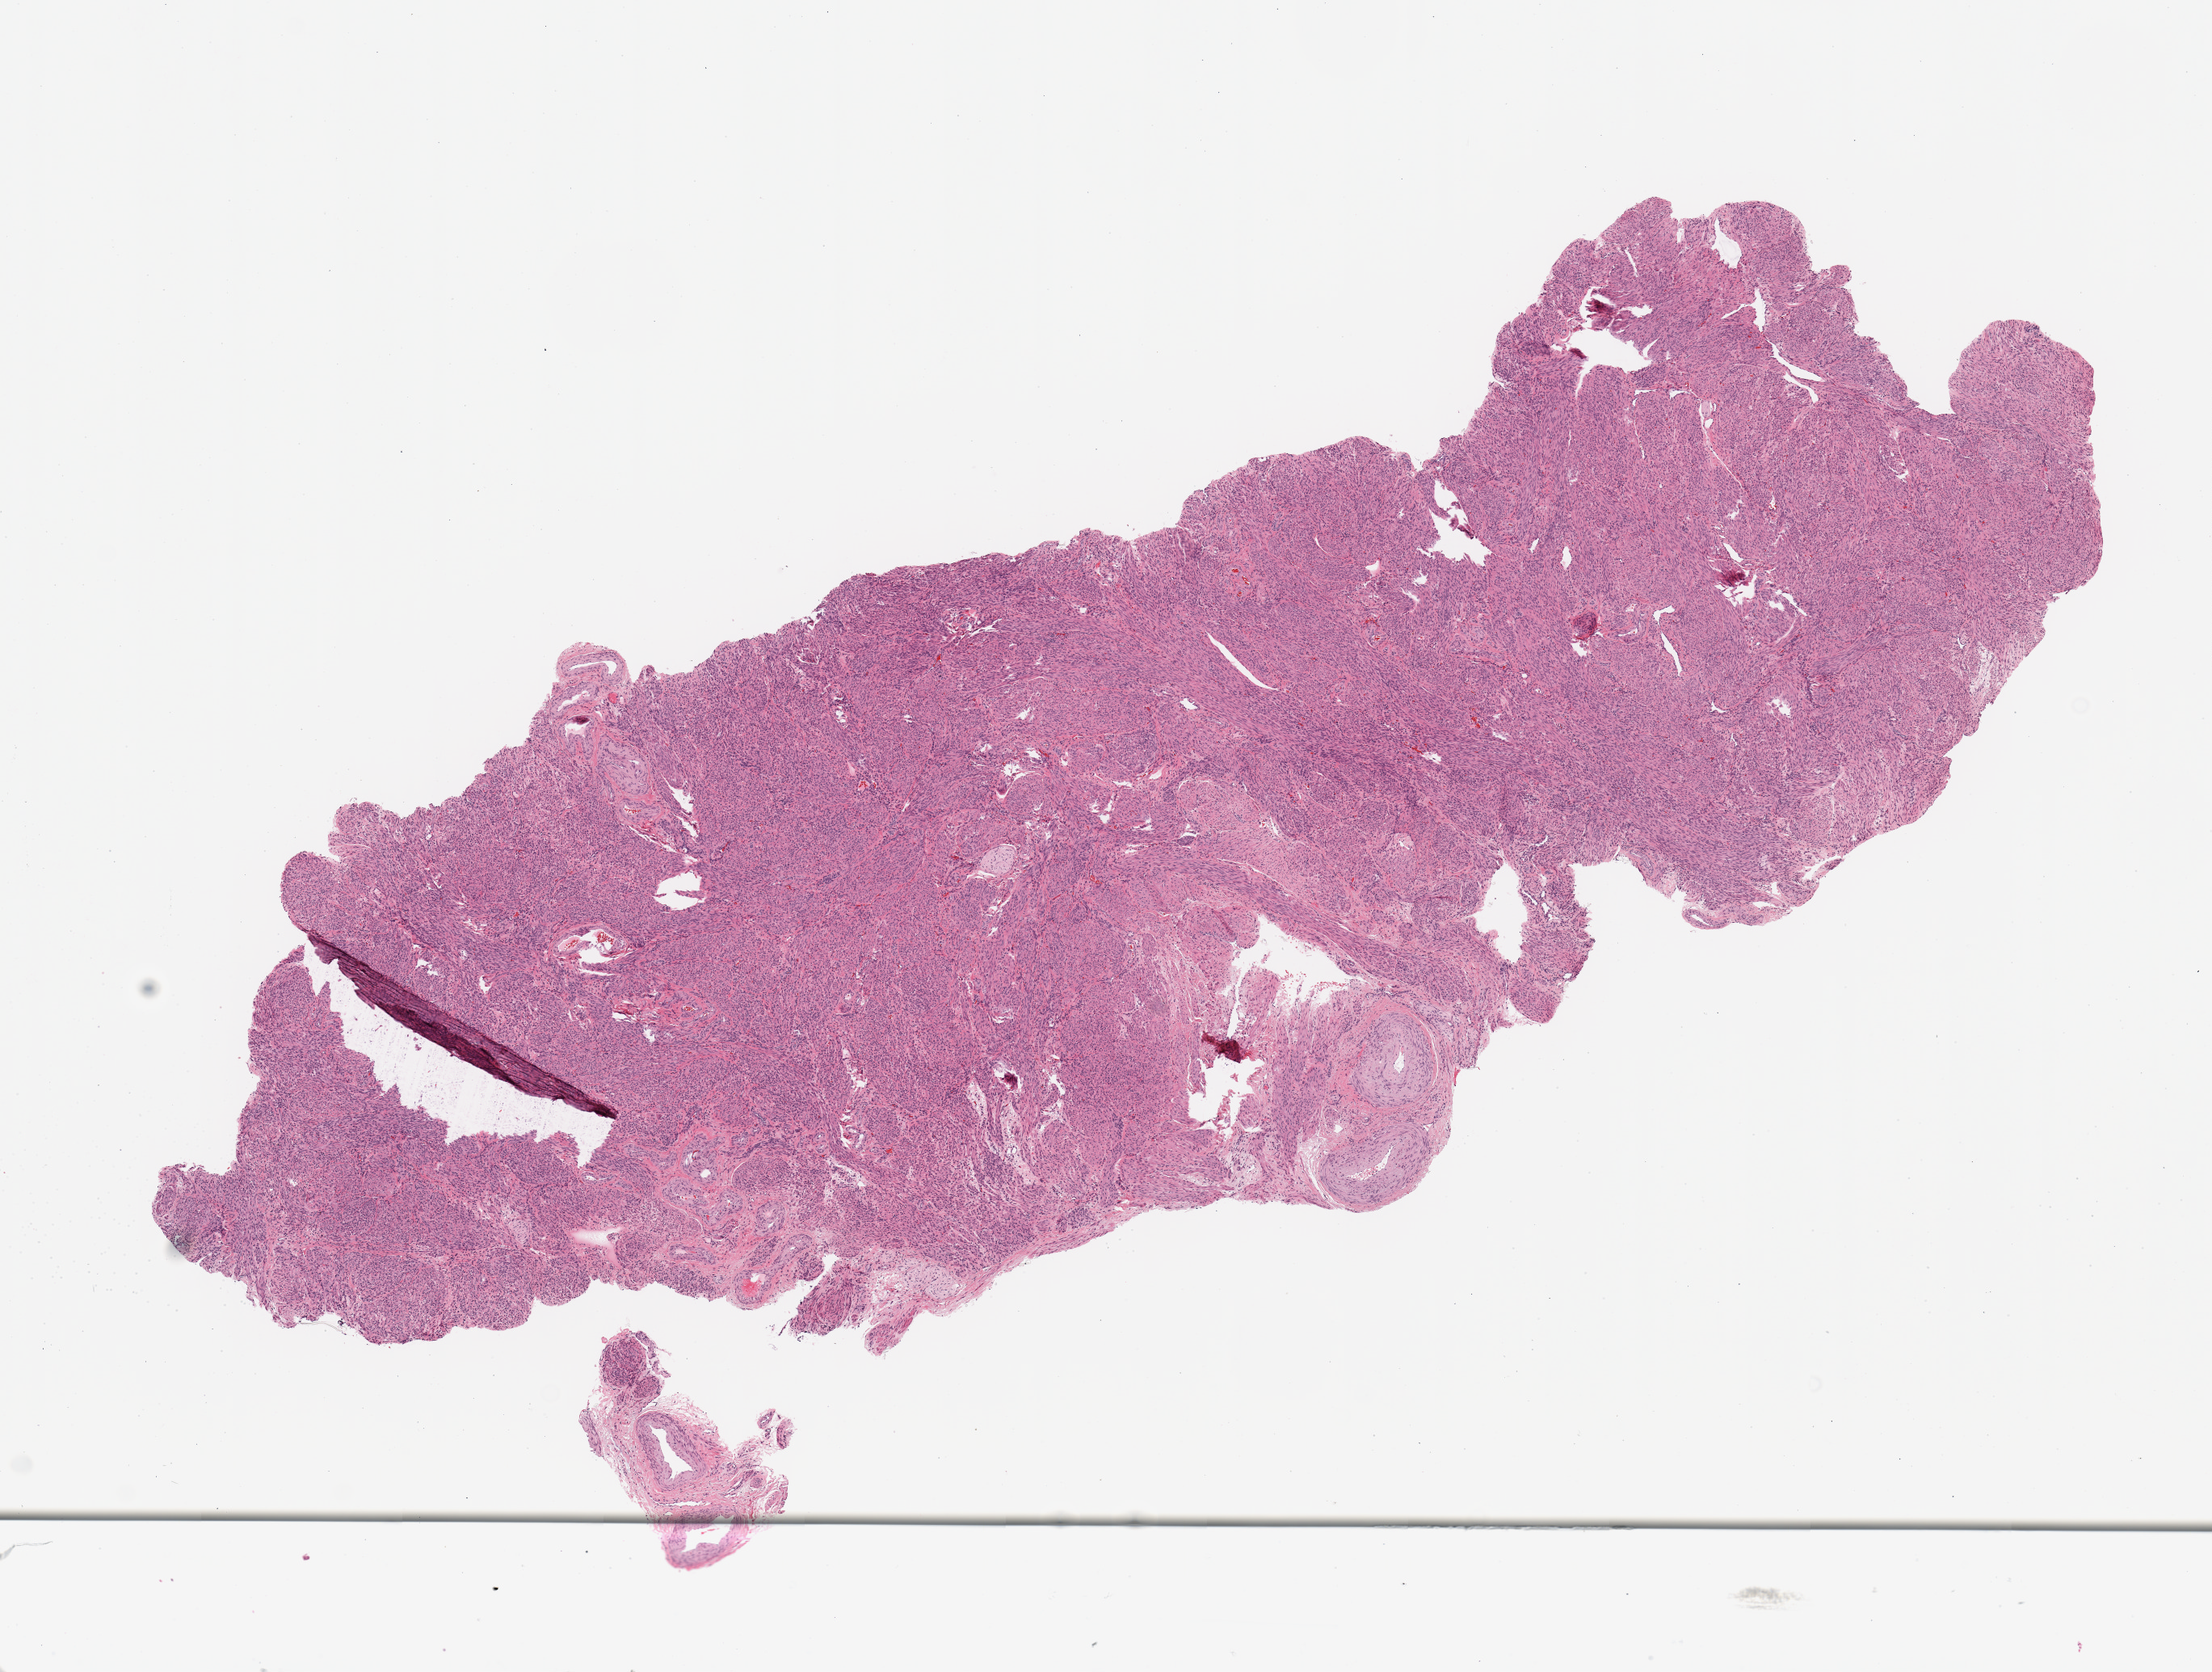
Digitized Hematoxylin and eosin (H&E) stained tissue section (whole slide) — a low-resolution overview of the entire scanned area, about 10.8 x 8.2 mm (from a 20x scan). Normal (non-tumour) tissue sample, uterus. Female, 58 y/o.
This section: normal (non-tumour) tissue from the same patient. Patient diagnosis: Endometrioid adenocarcinoma, NOS.